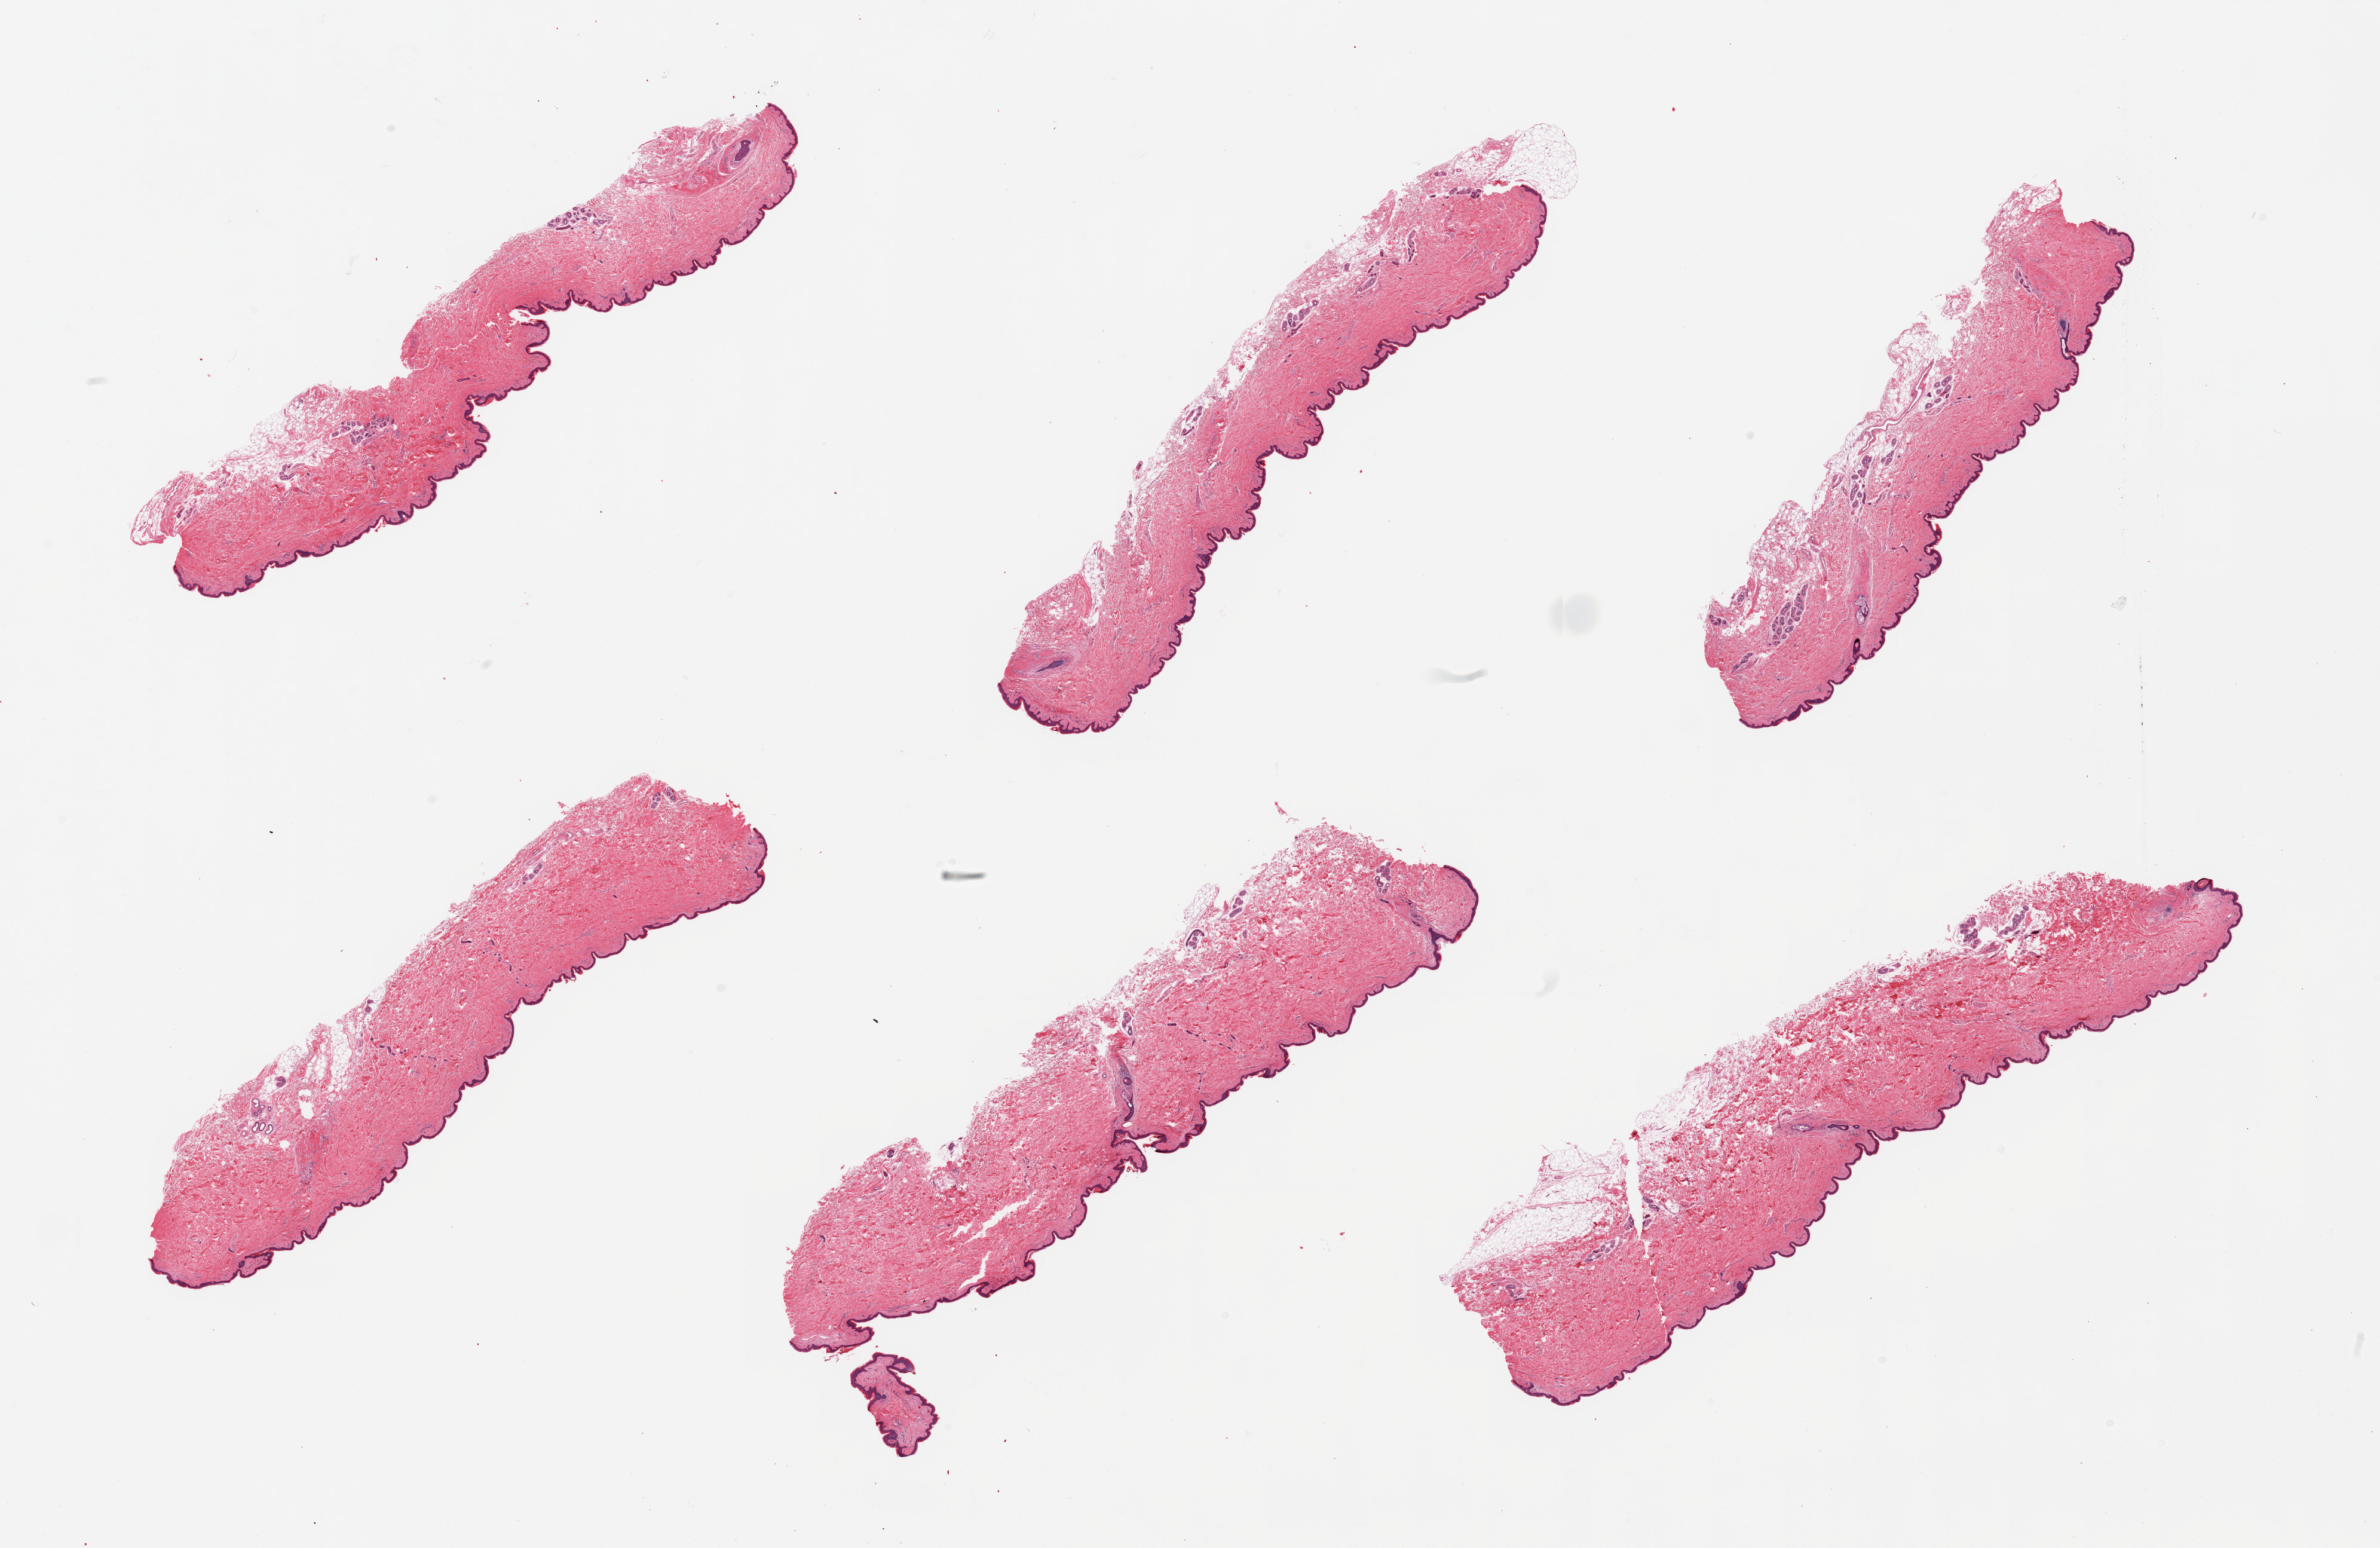
Digitized H&E-stained section, a low-resolution overview of the entire scanned area, about 31.5 x 20.5 mm, PAXgene-fixed paraffin-embedded (PFPE) section, target tissue: skin of suprapubic region, donor tissue sample. Donor sex: female.
Pathologist's review note for this sample: 6 pieces; well dissected.